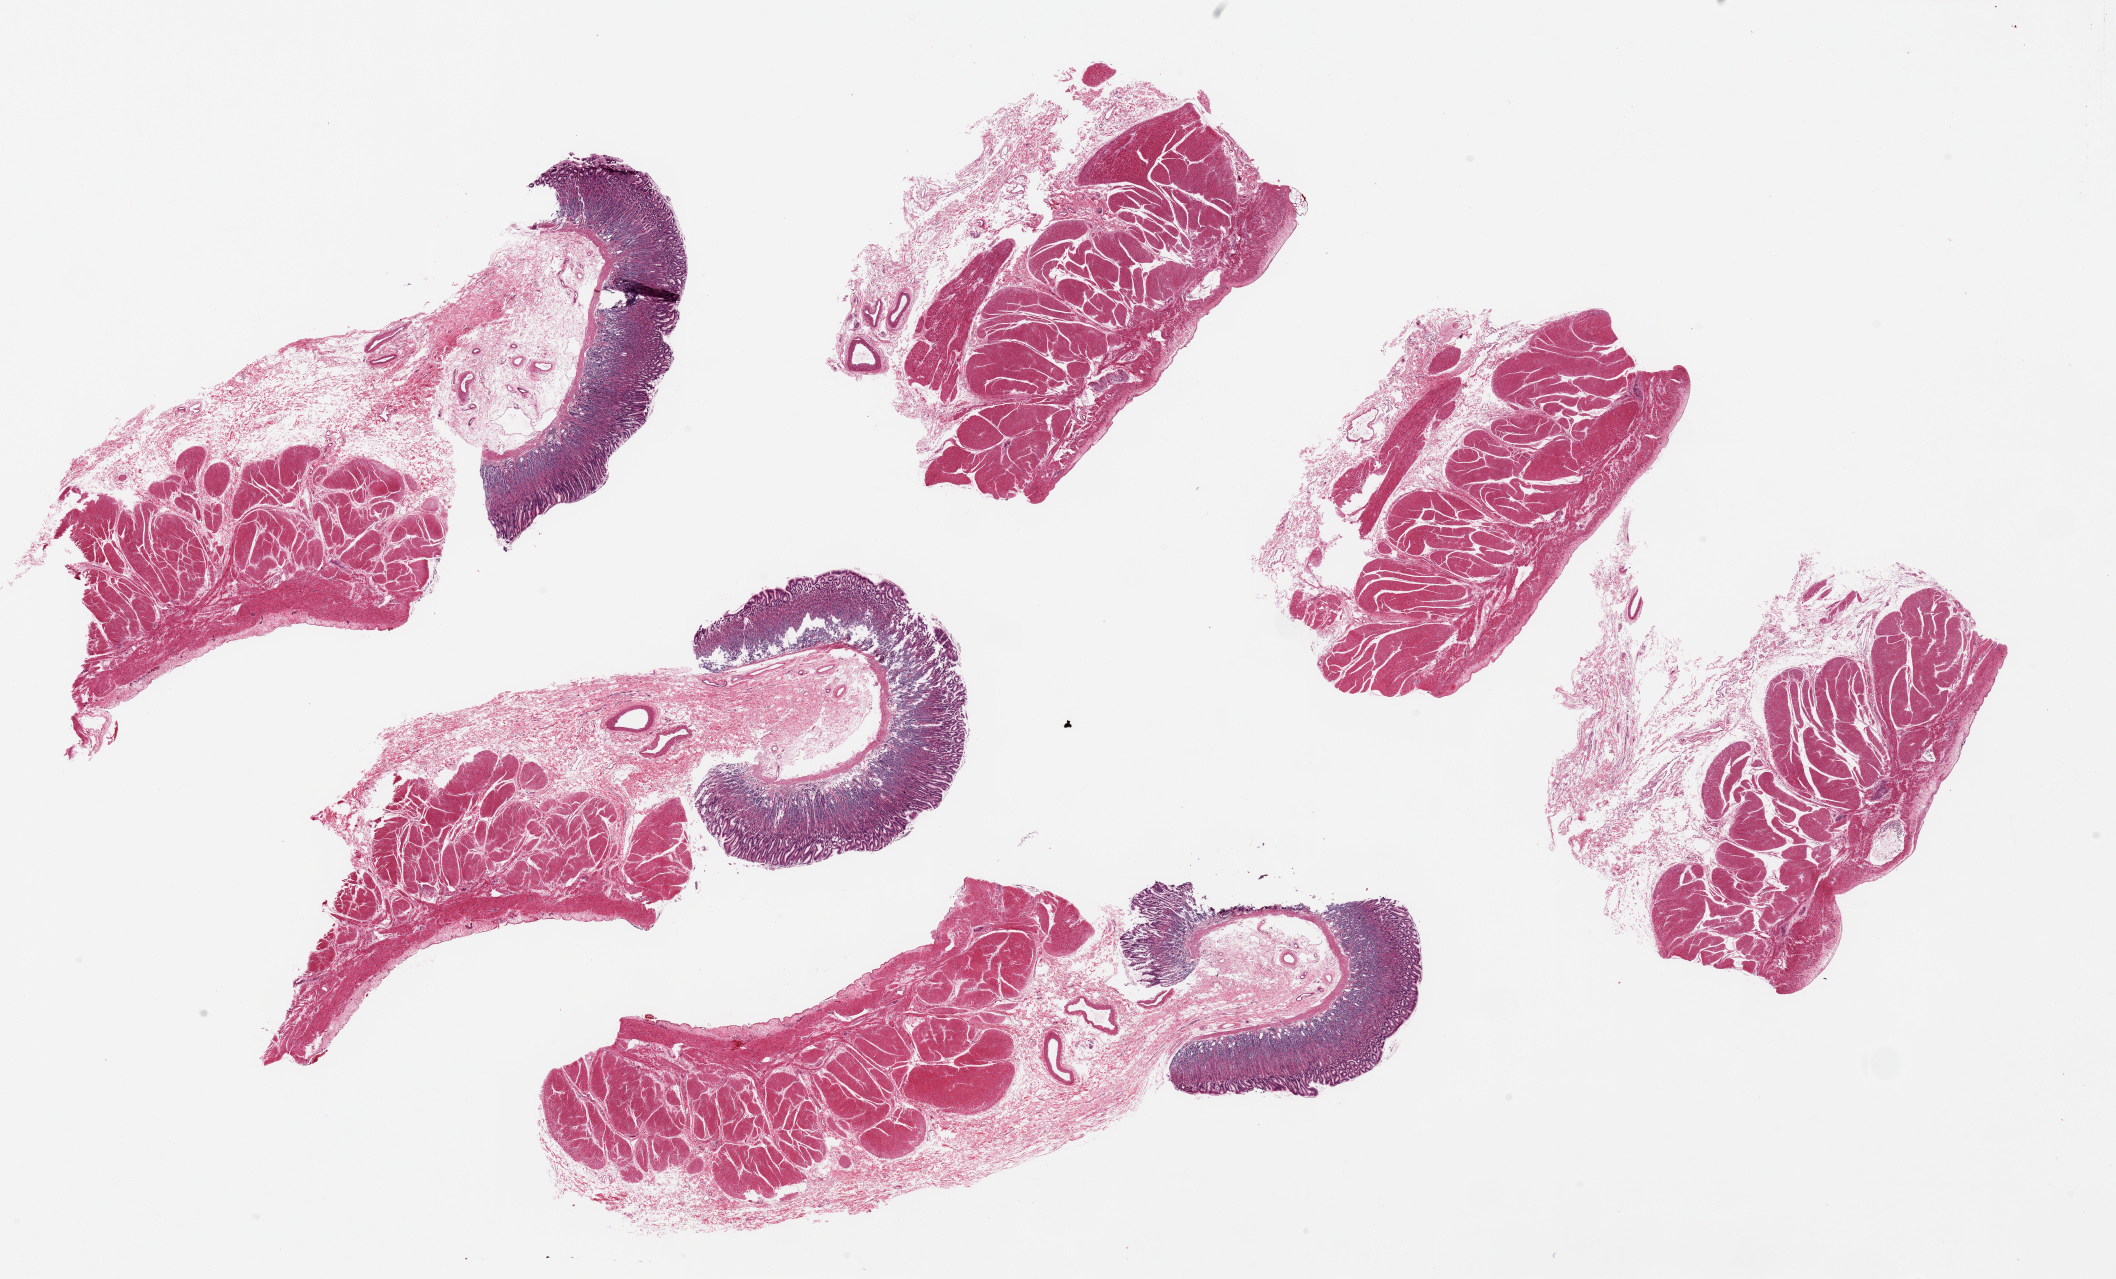
H&E whole-slide image — low-resolution overview of the scanned area, about 33.5 x 20.2 mm; PAXgene-fixed paraffin-embedded (PFPE) section; target tissue: stomach; donor tissue sample.
- reviewer comment on this tissue sample: 6 pieces; 3 with mucosa, ~1.2x5mm, well preserved